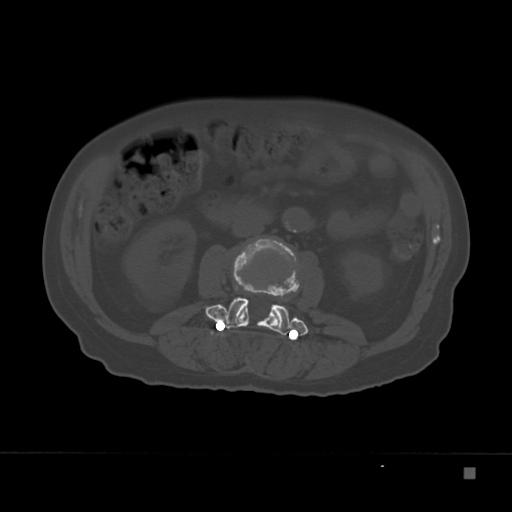
CT including the spine, one axial slice. Position 78 of 332 along the scan axis. Reconstruction kernel Br40s. Bone window (W 1800 / L 400 HU). 512 × 512 image matrix, field of view 389 × 389 mm. Patient: male, 72 years. Case-level facts recorded for this patient, not image findings: primary cancer: skeletal.
Annotated regions visible in this slice (semi-automatic segmentation, software-assisted and operator-edited):
- L2 vertebra: bounding box <233,237,296,328> (left, top, right, bottom; pixels)
- L3 vertebra: <205,272,309,336>